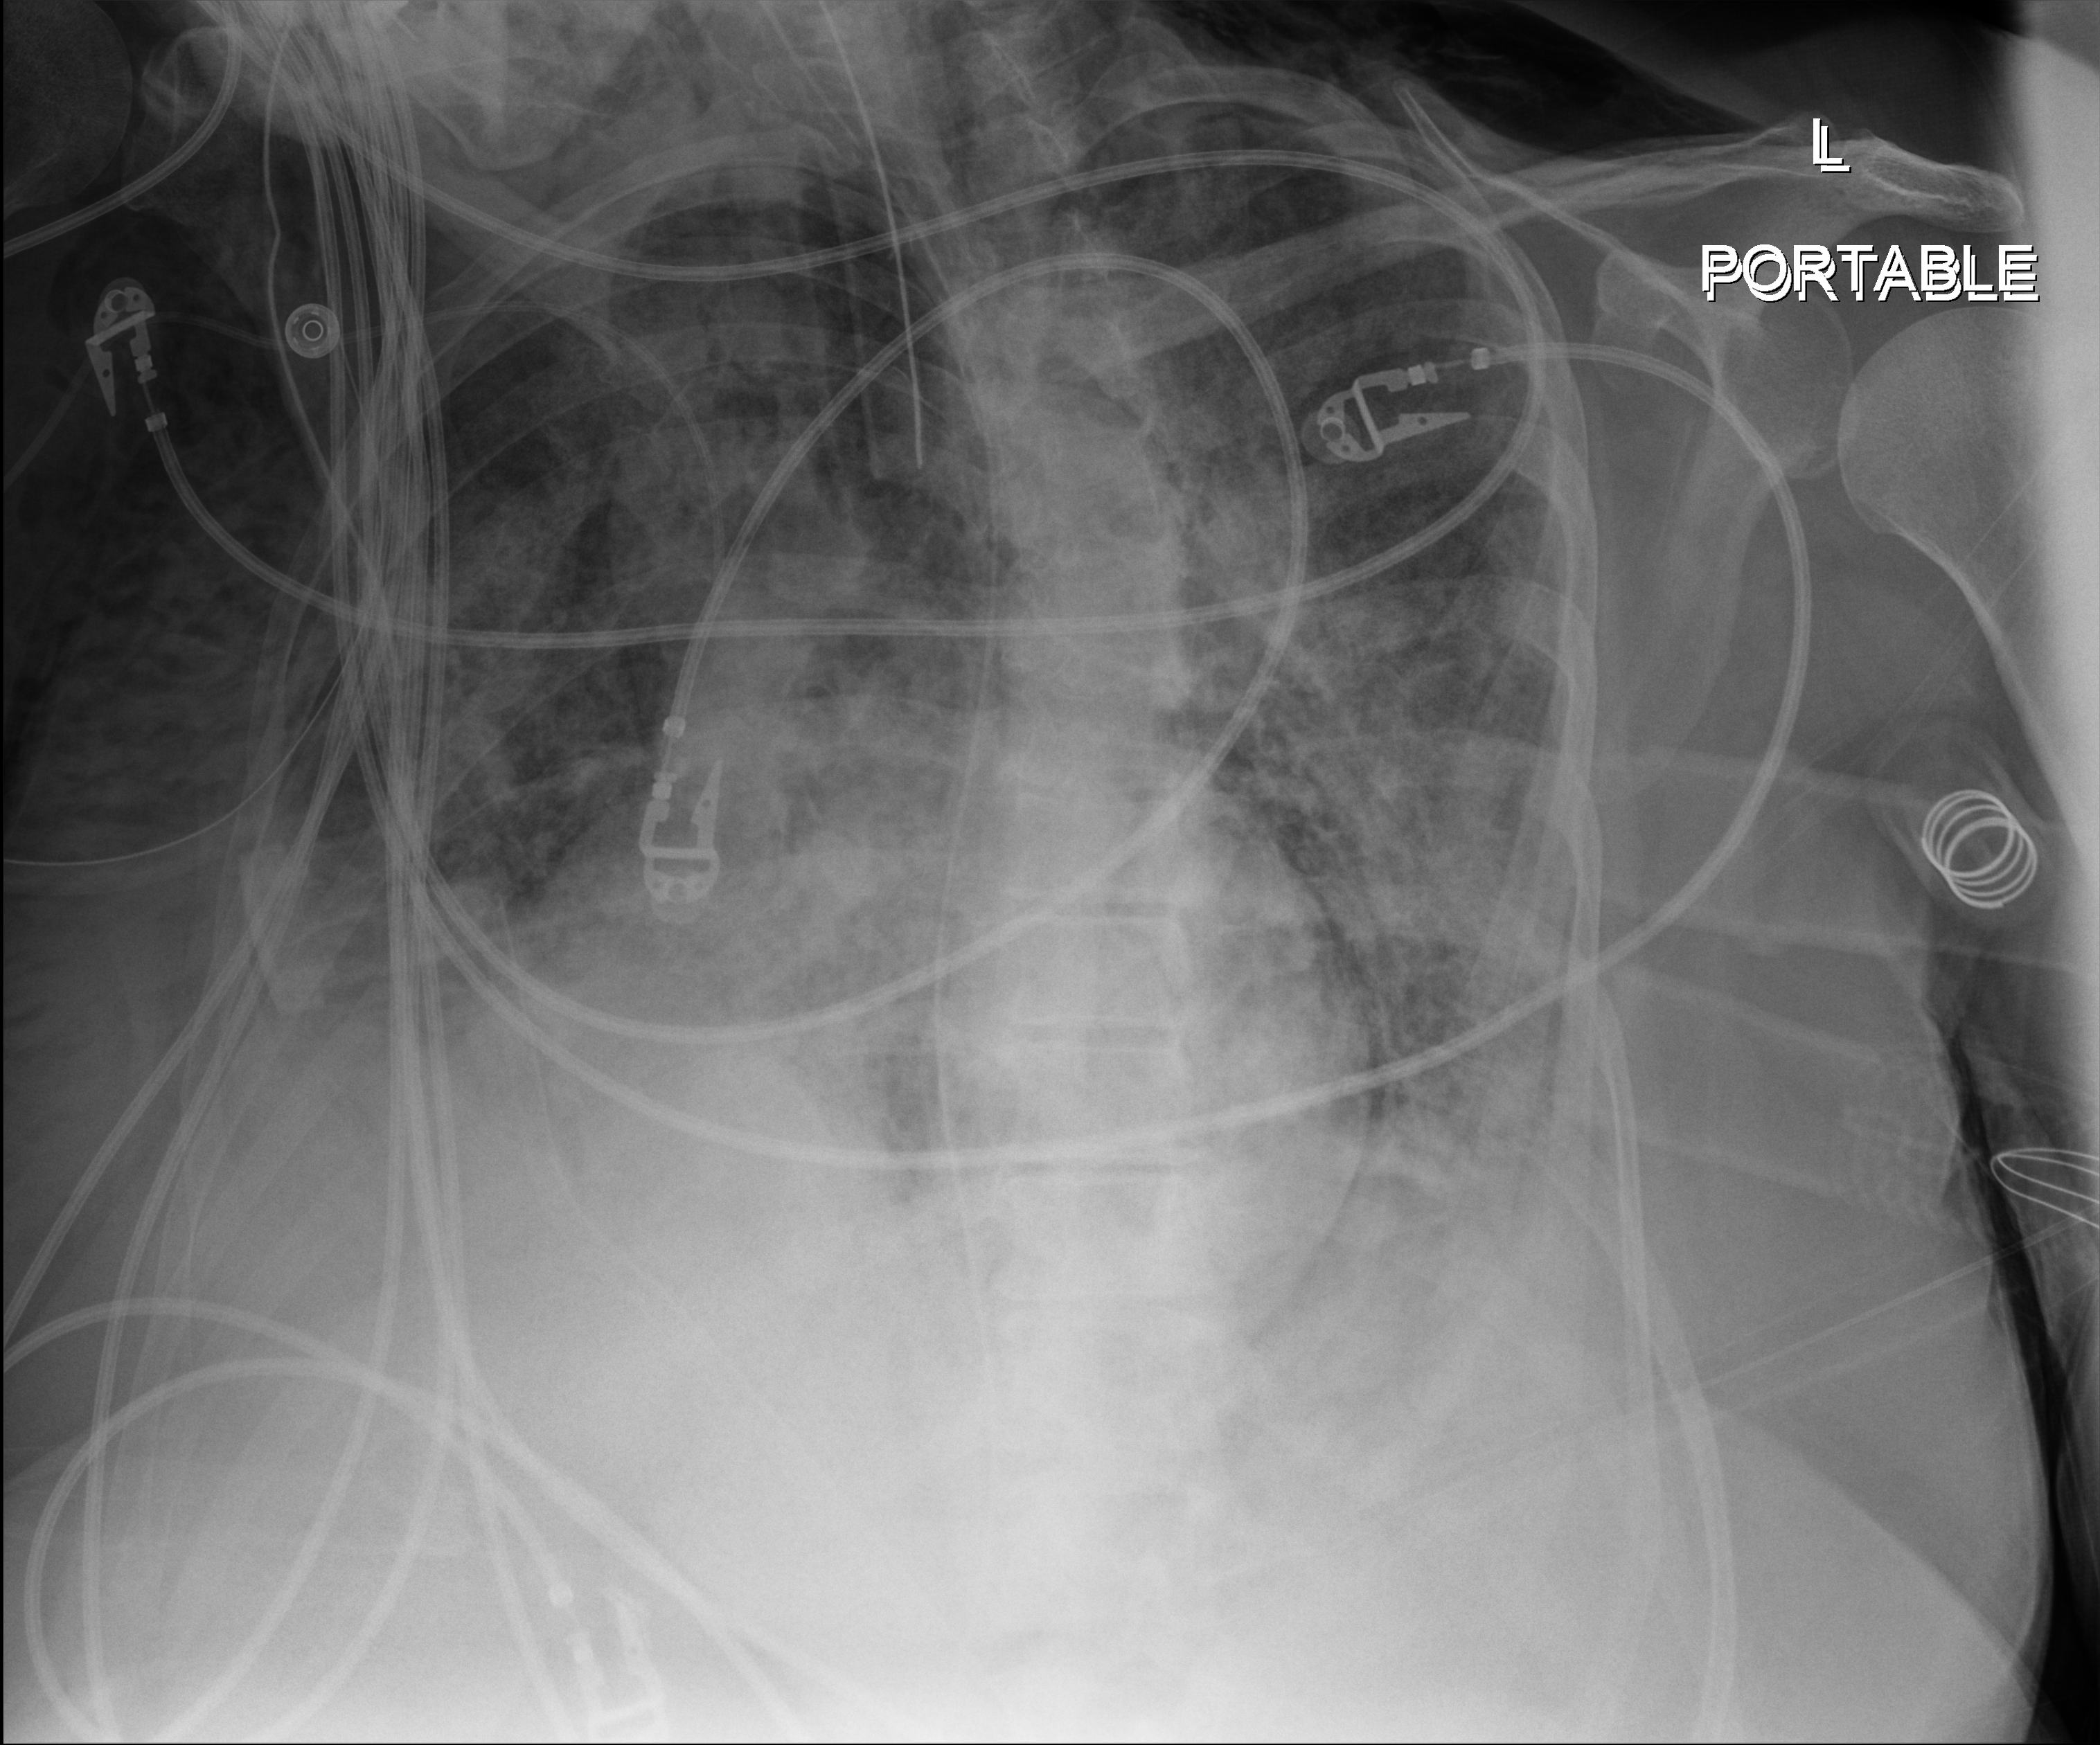
Portable chest radiograph. Patient hospitalised with COVID-19; female, aged 60–74 years.
Hospital-stay facts (about this admission, not read from this image; timing relative to this image not recorded): admitted to intensive care during this hospital stay: yes; mechanically ventilated during this hospital stay: yes.